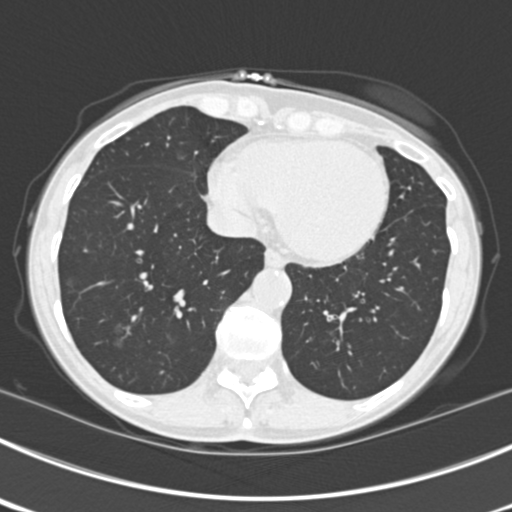
Axial slice from a low-dose chest CT screening exam; third screening round (two years after baseline); lung window (W 1500 / L -600 HU); 2 mm slice thickness; standard (soft-tissue) reconstruction kernel (B30f); 120 kVp; 512 × 512 image matrix. Female participant, aged 63 years at enrolment. Current smoker at enrolment.
Expert-annotated lung lesion, bounding box [x1, y1, x2, y2] px = [103, 310, 148, 356]. The screening reader recorded 9 non-calcified nodules or masses ≥4 mm on this exam (left upper lobe, right upper lobe, left upper lobe, left lower lobe, right middle lobe, left lower lobe, left lower lobe, right lower lobe, right lower lobe); which of them this box marks is not recorded. Lung cancer was diagnosed 15 days after this screen: bronchiolo-alveolar adenocarcinoma, NOS, right upper lobe, right middle lobe, right lower lobe, left upper lobe, left lower lobe, moderately differentiated (G2), stage IV (AJCC 6th edition).